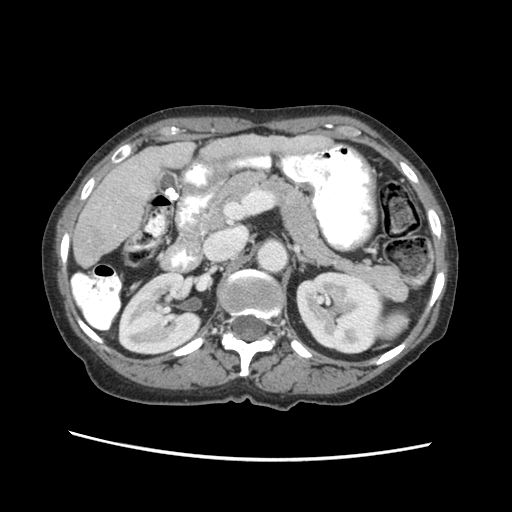
Contrast-enhanced abdominal CT (liver protocol), one axial slice; position 21 of 63 along the scan axis; reconstruction kernel STANDARD; 120 kVp; soft-tissue window (W 400 / L 40 HU); 2.5 mm slice thickness; 512 × 512 image matrix, field of view 340 × 340 mm. From the clinical record (not read from this slice): diagnosis: hepatocellular carcinoma (patient treated with transarterial chemoembolisation; whether this scan precedes or follows treatment is not stated here); TNM stage (as recorded): Stage-I; Child-Pugh class: B; tumour differentiation: well differentiated.
Outlined on this slice (semi-automatic segmentation, software-assisted and operator-edited):
- liver parenchyma outside the tumour (the mass and vessels are separate outlines, so this box may not span the whole liver): bounding box <72,130,326,265> (left, top, right, bottom; pixels)